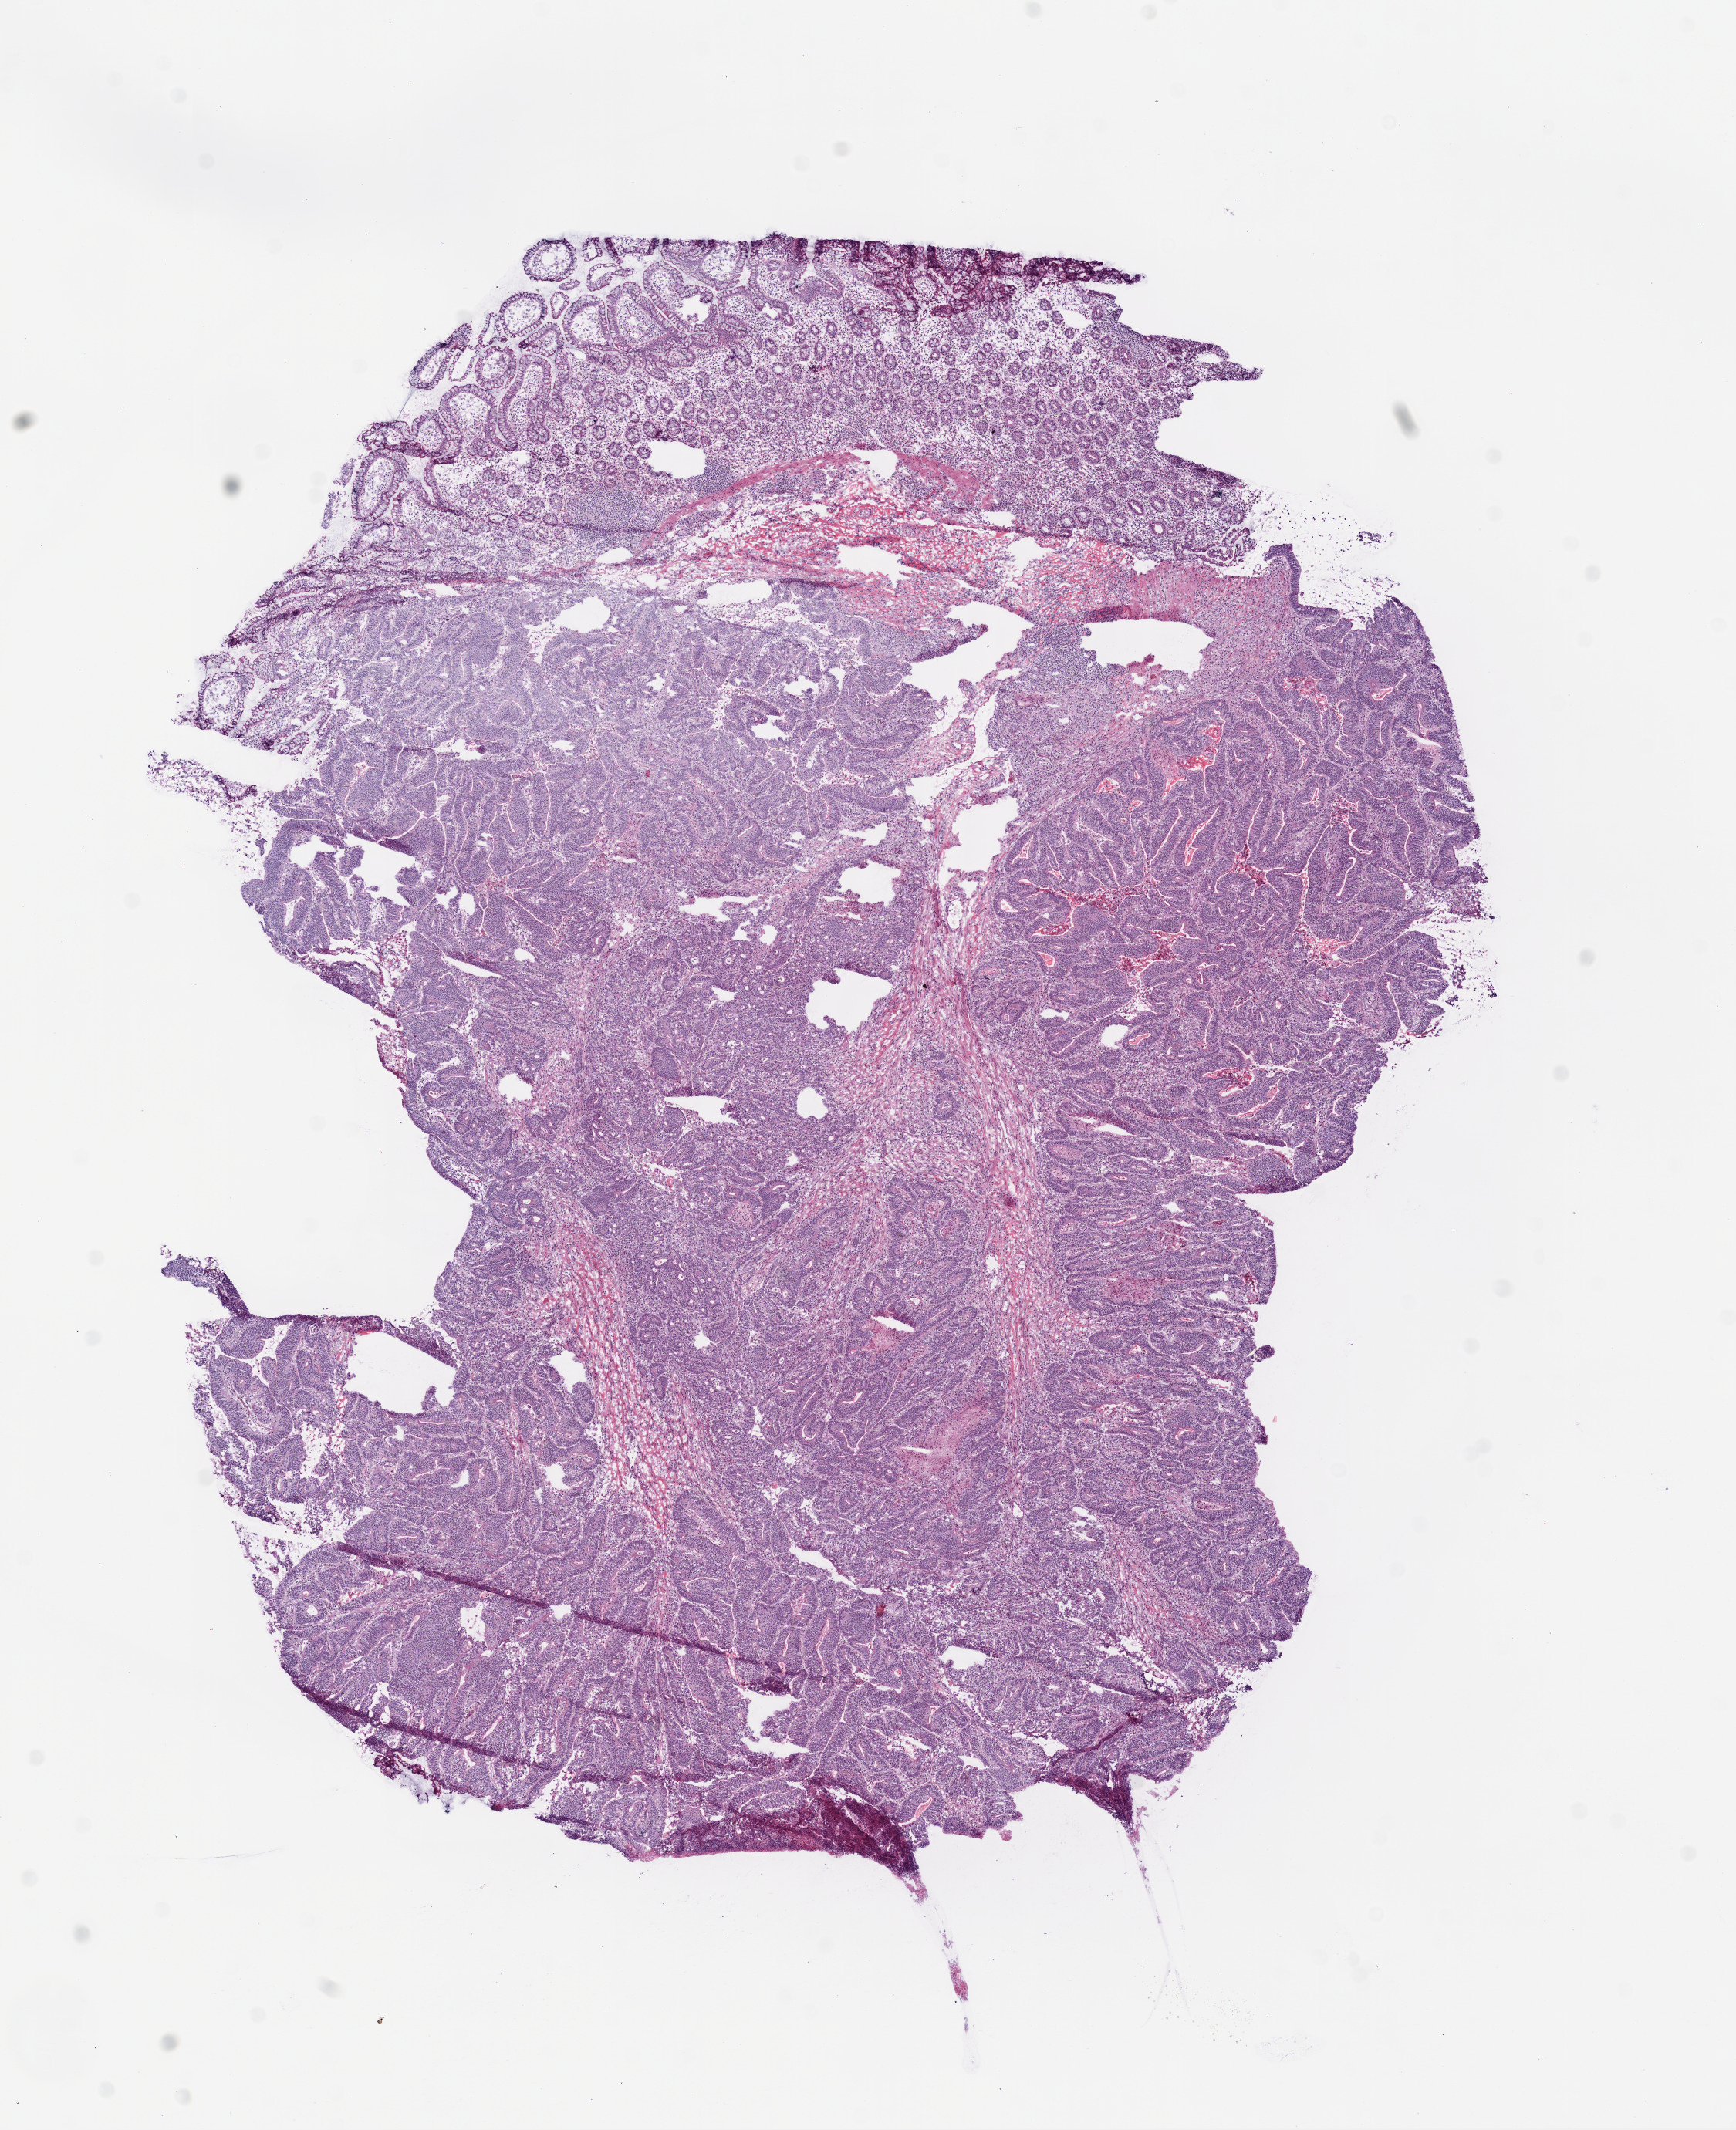
Digitized Hematoxylin and eosin (H&E) stained tissue section (whole slide) — shown as a low-resolution overview of the whole scanned area (about 9.0 x 11.1 mm), frozen section from the top of the tissue portion, primary tumour sample from the colon. Patient: female, age at initial diagnosis 65 years. Pathologist review of this section (percent, as recorded): tumour cells 67%, tumour nuclei 70%, normal cells 15%, stromal cells 10%, necrosis 8%.
Histologic diagnosis: Adenocarcinoma, NOS (cecum). AJCC pathologic stage: IIA. Lymph nodes positive (case pathology): 0 of 20 examined.